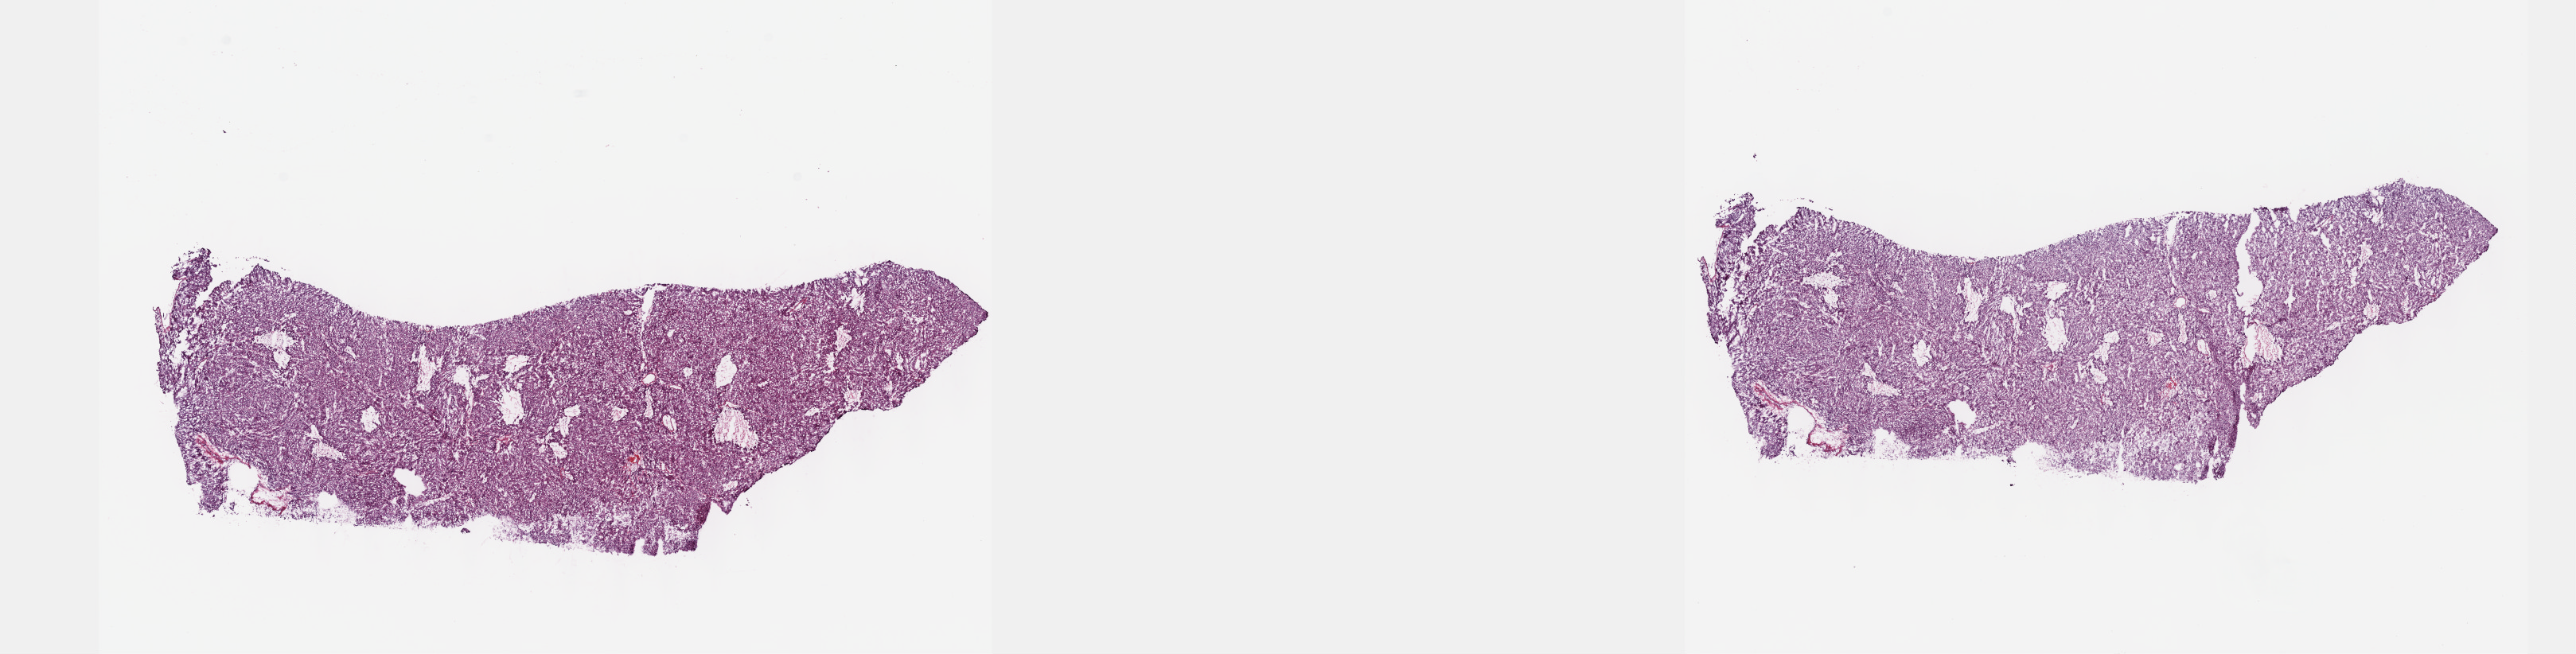
Digitized H&E-stained tissue section (whole slide), shown as a low-resolution overview of the whole scanned area (about 26.2 x 6.6 mm); frozen section; primary tumour sample from the liver. Male patient; age at initial diagnosis 76 years.
Pathologic diagnosis: Hepatocellular carcinoma, NOS.